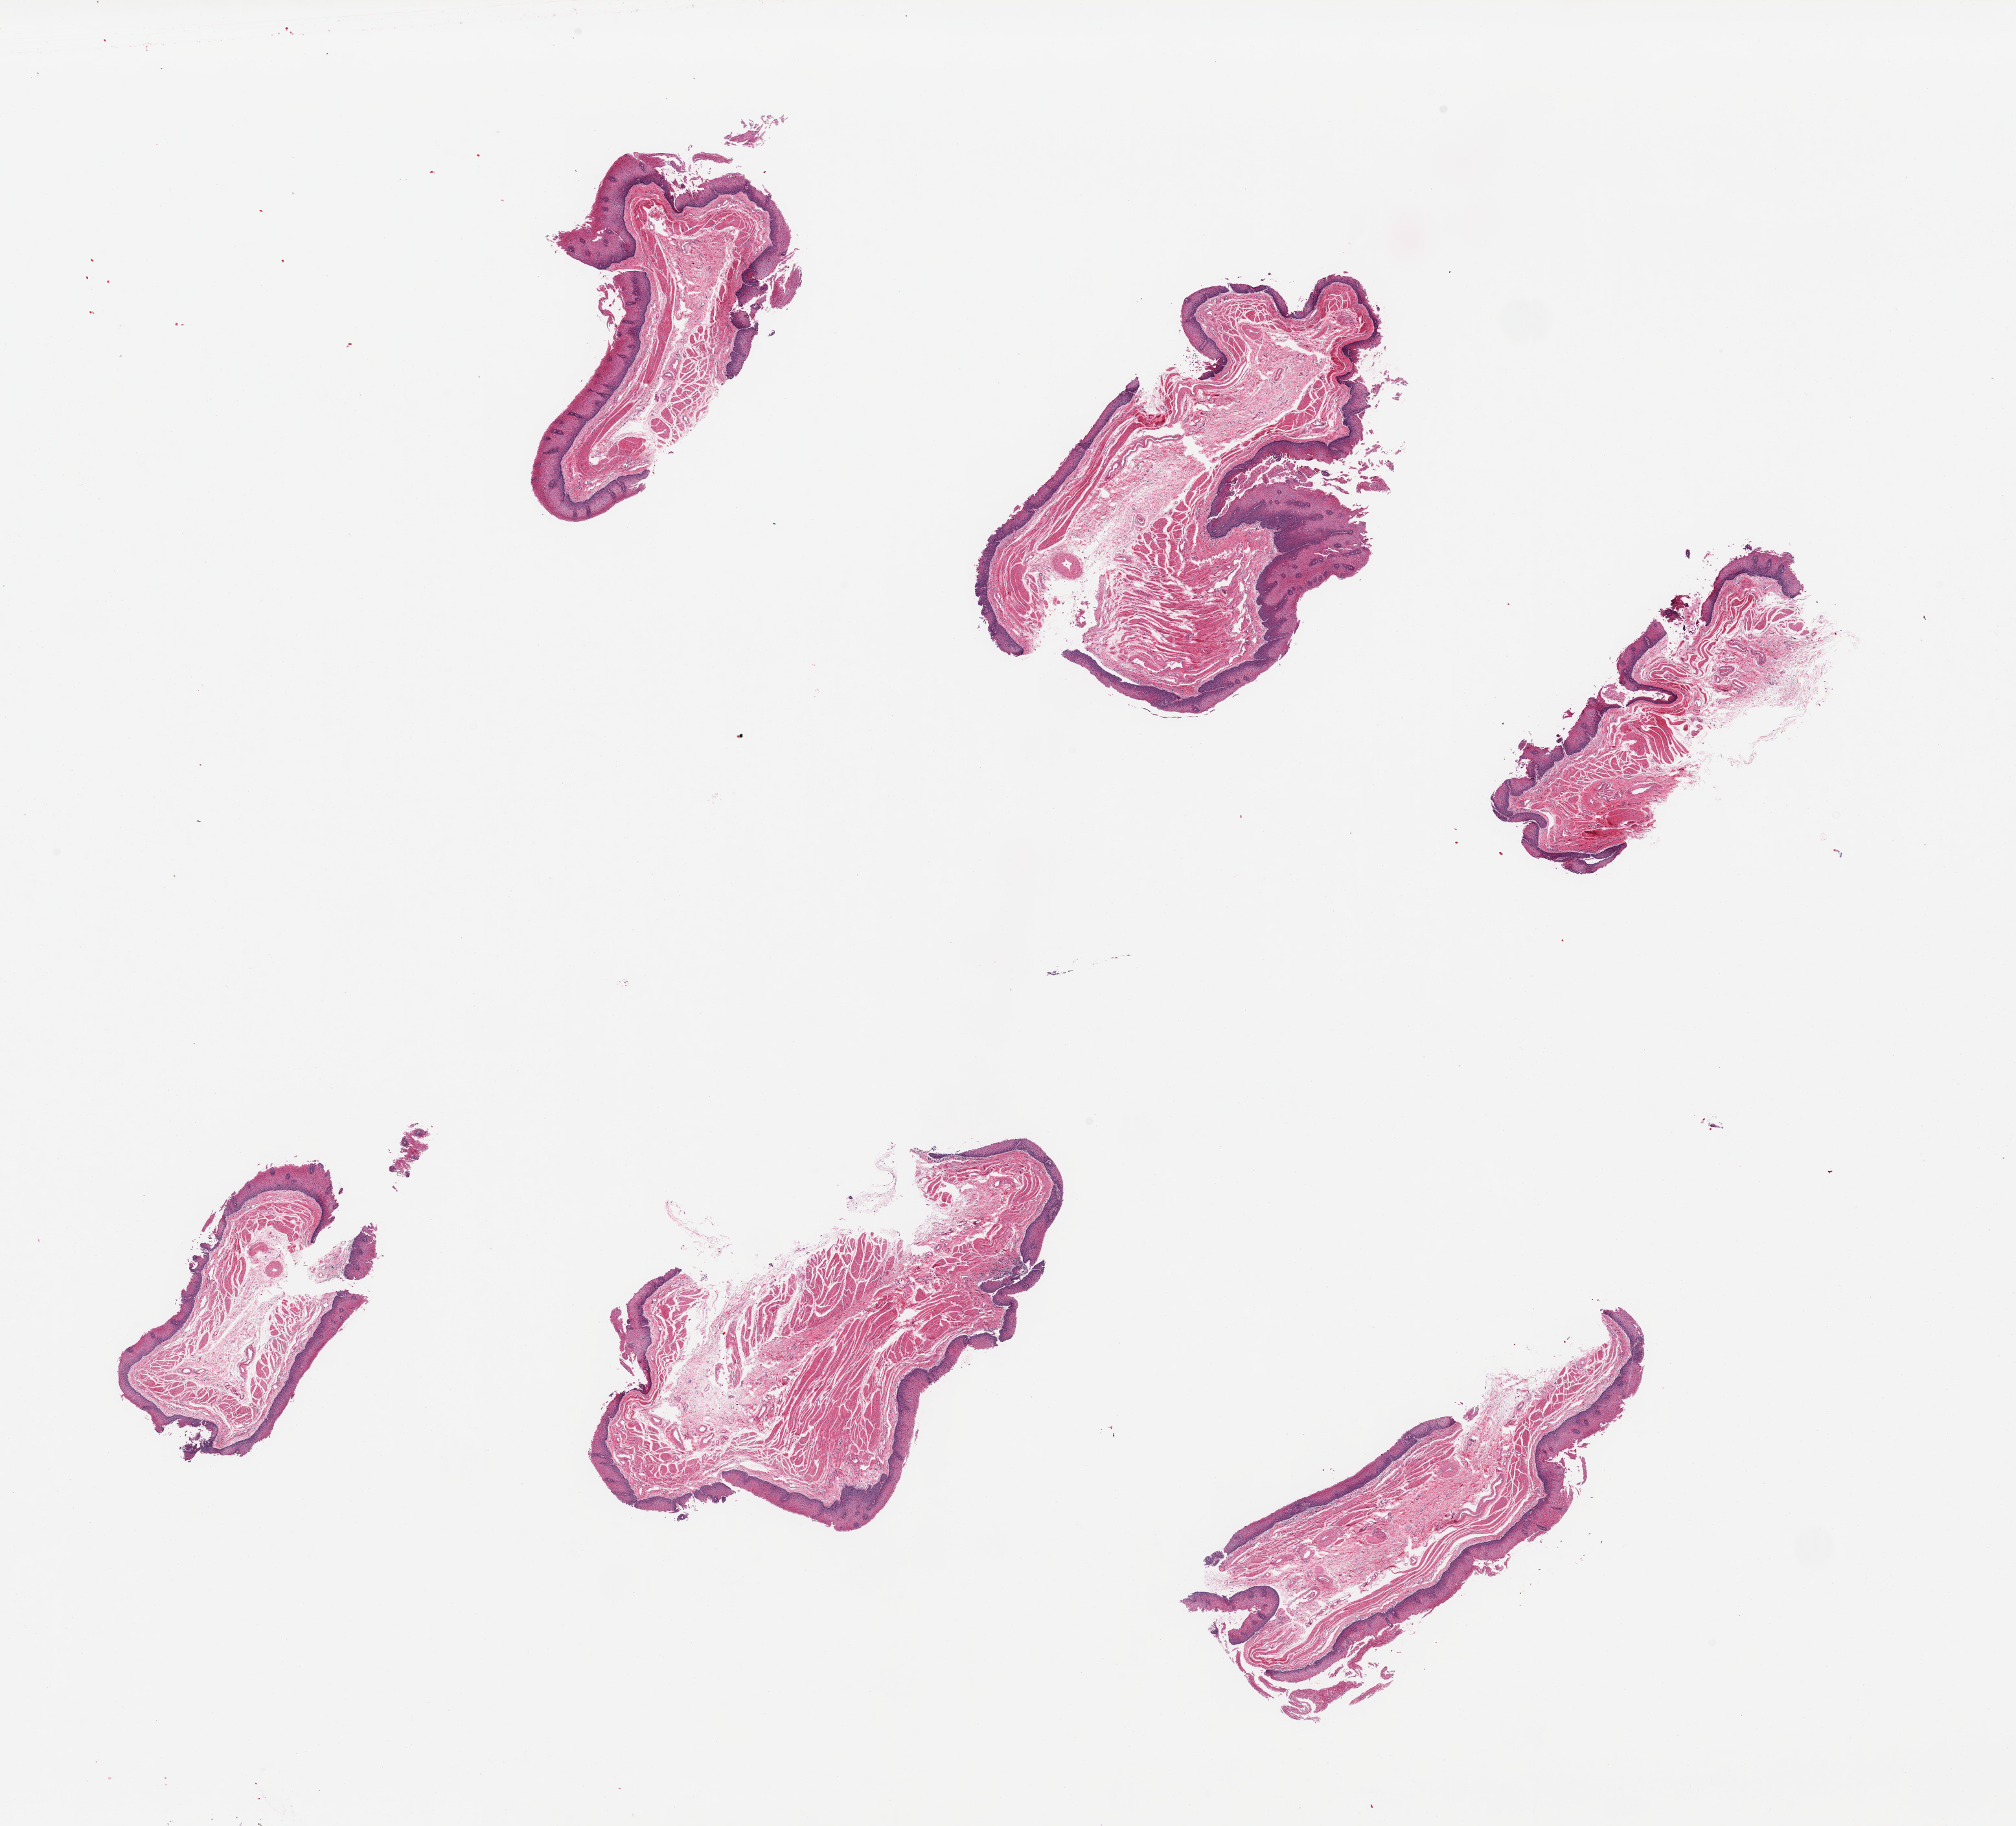
Whole-slide image, haematoxylin and eosin stain, brightfield — low-resolution overview of the scanned area, about 24.6 x 22.3 mm (from a 20x scan). PAXgene-fixed, paraffin-embedded tissue. Sampled site (target tissue): esophageal mucous membrane. Tissue donor sample. Female donor.
* reviewer comment on this tissue sample: 6 pieces partially sloughed epithelium